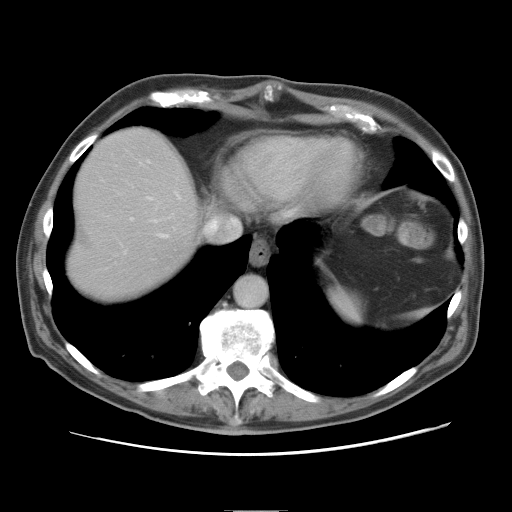
Contrast-enhanced abdominal CT, one axial slice. Position 70 of 89 along the scan axis. 120 kVp. Intravenous contrast given. Soft-tissue window (W 400 / L 40 HU). 5 mm slice thickness. 512 × 512 image matrix, field of view 375 × 375 mm. Male patient, age 69 years. From the clinical record (not read from this slice): diagnosis: colorectal cancer liver metastases, imaged before liver resection; multiple liver metastases: no; largest metastasis: 8.5 cm; disease in both lobes: no.
Annotated regions visible in this slice (manually delineated by an expert):
- hepatic veins: bounding box (x1, y1, x2, y2) in pixels: (145, 189, 240, 240)
- liver: (66, 129, 200, 300)
- planned liver remnant (the part of the liver to remain after resection): (66, 129, 200, 302)
- portal vein (with intrahepatic branches): (130, 217, 158, 223)